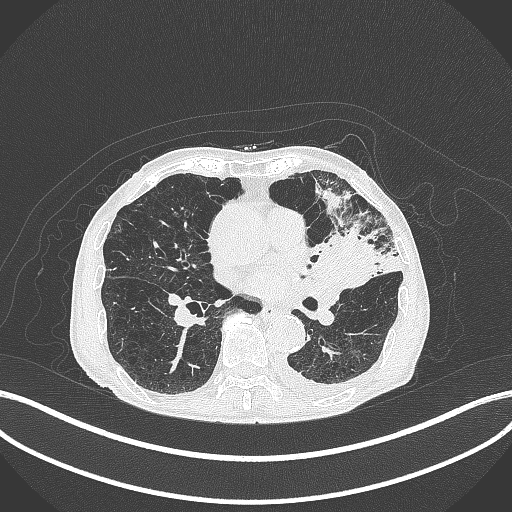
Chest CT, one axial slice. Slice 185 of 385 in the series (ordered by position). Lung window (W 1500 / L -600 HU). 1 mm slice thickness. 512 × 512 image matrix, field of view 400 × 400 mm. Male patient, age 90 years or older. Case-level facts recorded for this patient, not image findings: clinical TNM (as recorded): T2b N1 M0.
Structures marked on this image (bounding box drawn by a radiologist):
- lung tumour (recorded histology: squamous cell carcinoma): bounding box [x1, y1, x2, y2] px = [312, 233, 379, 291]